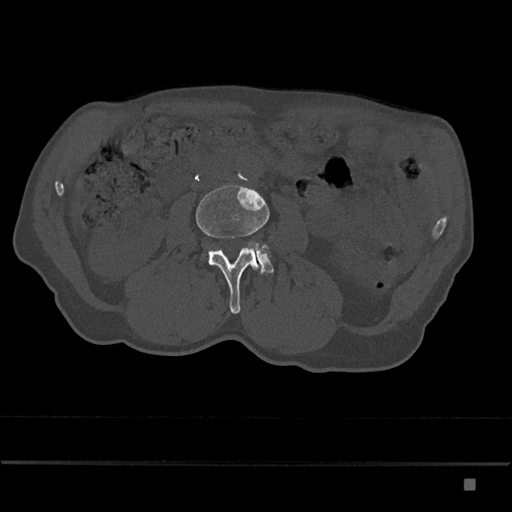
CT including the spine, one axial slice. Slice 393 of 797 in the series (ordered by position). 120 kVp. Bone window (W 1800 / L 400 HU). 512 × 512 image matrix, field of view 390 × 390 mm. Male patient, age 72 years. Case-level facts recorded for this patient, not image findings: primary cancer: prostate.
Structures marked on this image (semi-automatically segmented with operator editing):
- L3 vertebra: bounding box <196,185,270,314> (left, top, right, bottom; pixels)
- L4 vertebra: <248,244,274,274>